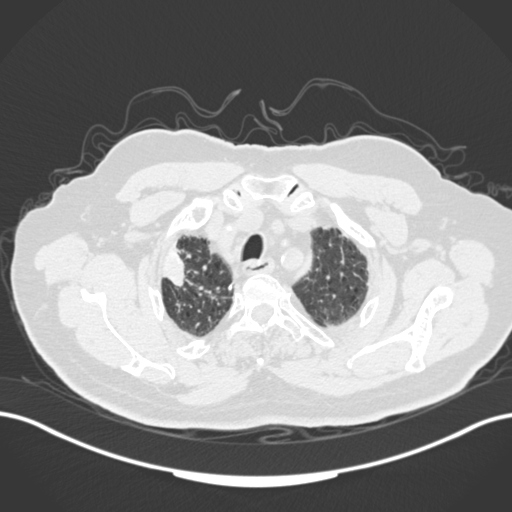
Chest CT, one axial slice. Slice 146 of 205 in the series (ordered by position). Lung window (W 1500 / L -600 HU). 512 × 512 image matrix. Male patient, age 72 years. Case-level facts recorded for this patient, not image findings: clinical TNM (as recorded): T1a N0 M0.
Annotated regions visible in this slice (bounding box drawn by a radiologist):
- lung tumour (recorded histology: squamous cell carcinoma): bounding box (x1, y1, x2, y2) in pixels: (162, 240, 188, 288)